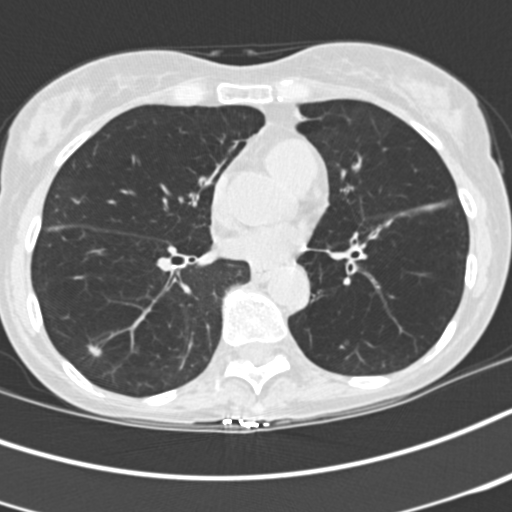
Low-dose screening chest CT, axial slice, first (baseline) screen, lung window (W 1500 / L -600 HU), 2 mm slice thickness, slice 101 of 197 in the series, 512 × 512 image matrix, field of view 280 × 280 mm. Female, age 68 years at enrolment.
Expert reader's lesion annotation, bounding box (x1, y1, x2, y2) in pixels: (73, 337, 113, 367). The exam's reader record, not a measurement of the box and not confirmed to be the same lesion: non-calcified nodule or mass ≥4 mm, right lower lobe, 8 × 4 mm, spiculated (stellate) margins, soft tissue attenuation. Lung cancer was diagnosed 1012 days after this screen (after the third annual screen): squamous cell carcinoma, NOS, right lower lobe, stage IA (AJCC 6th edition).